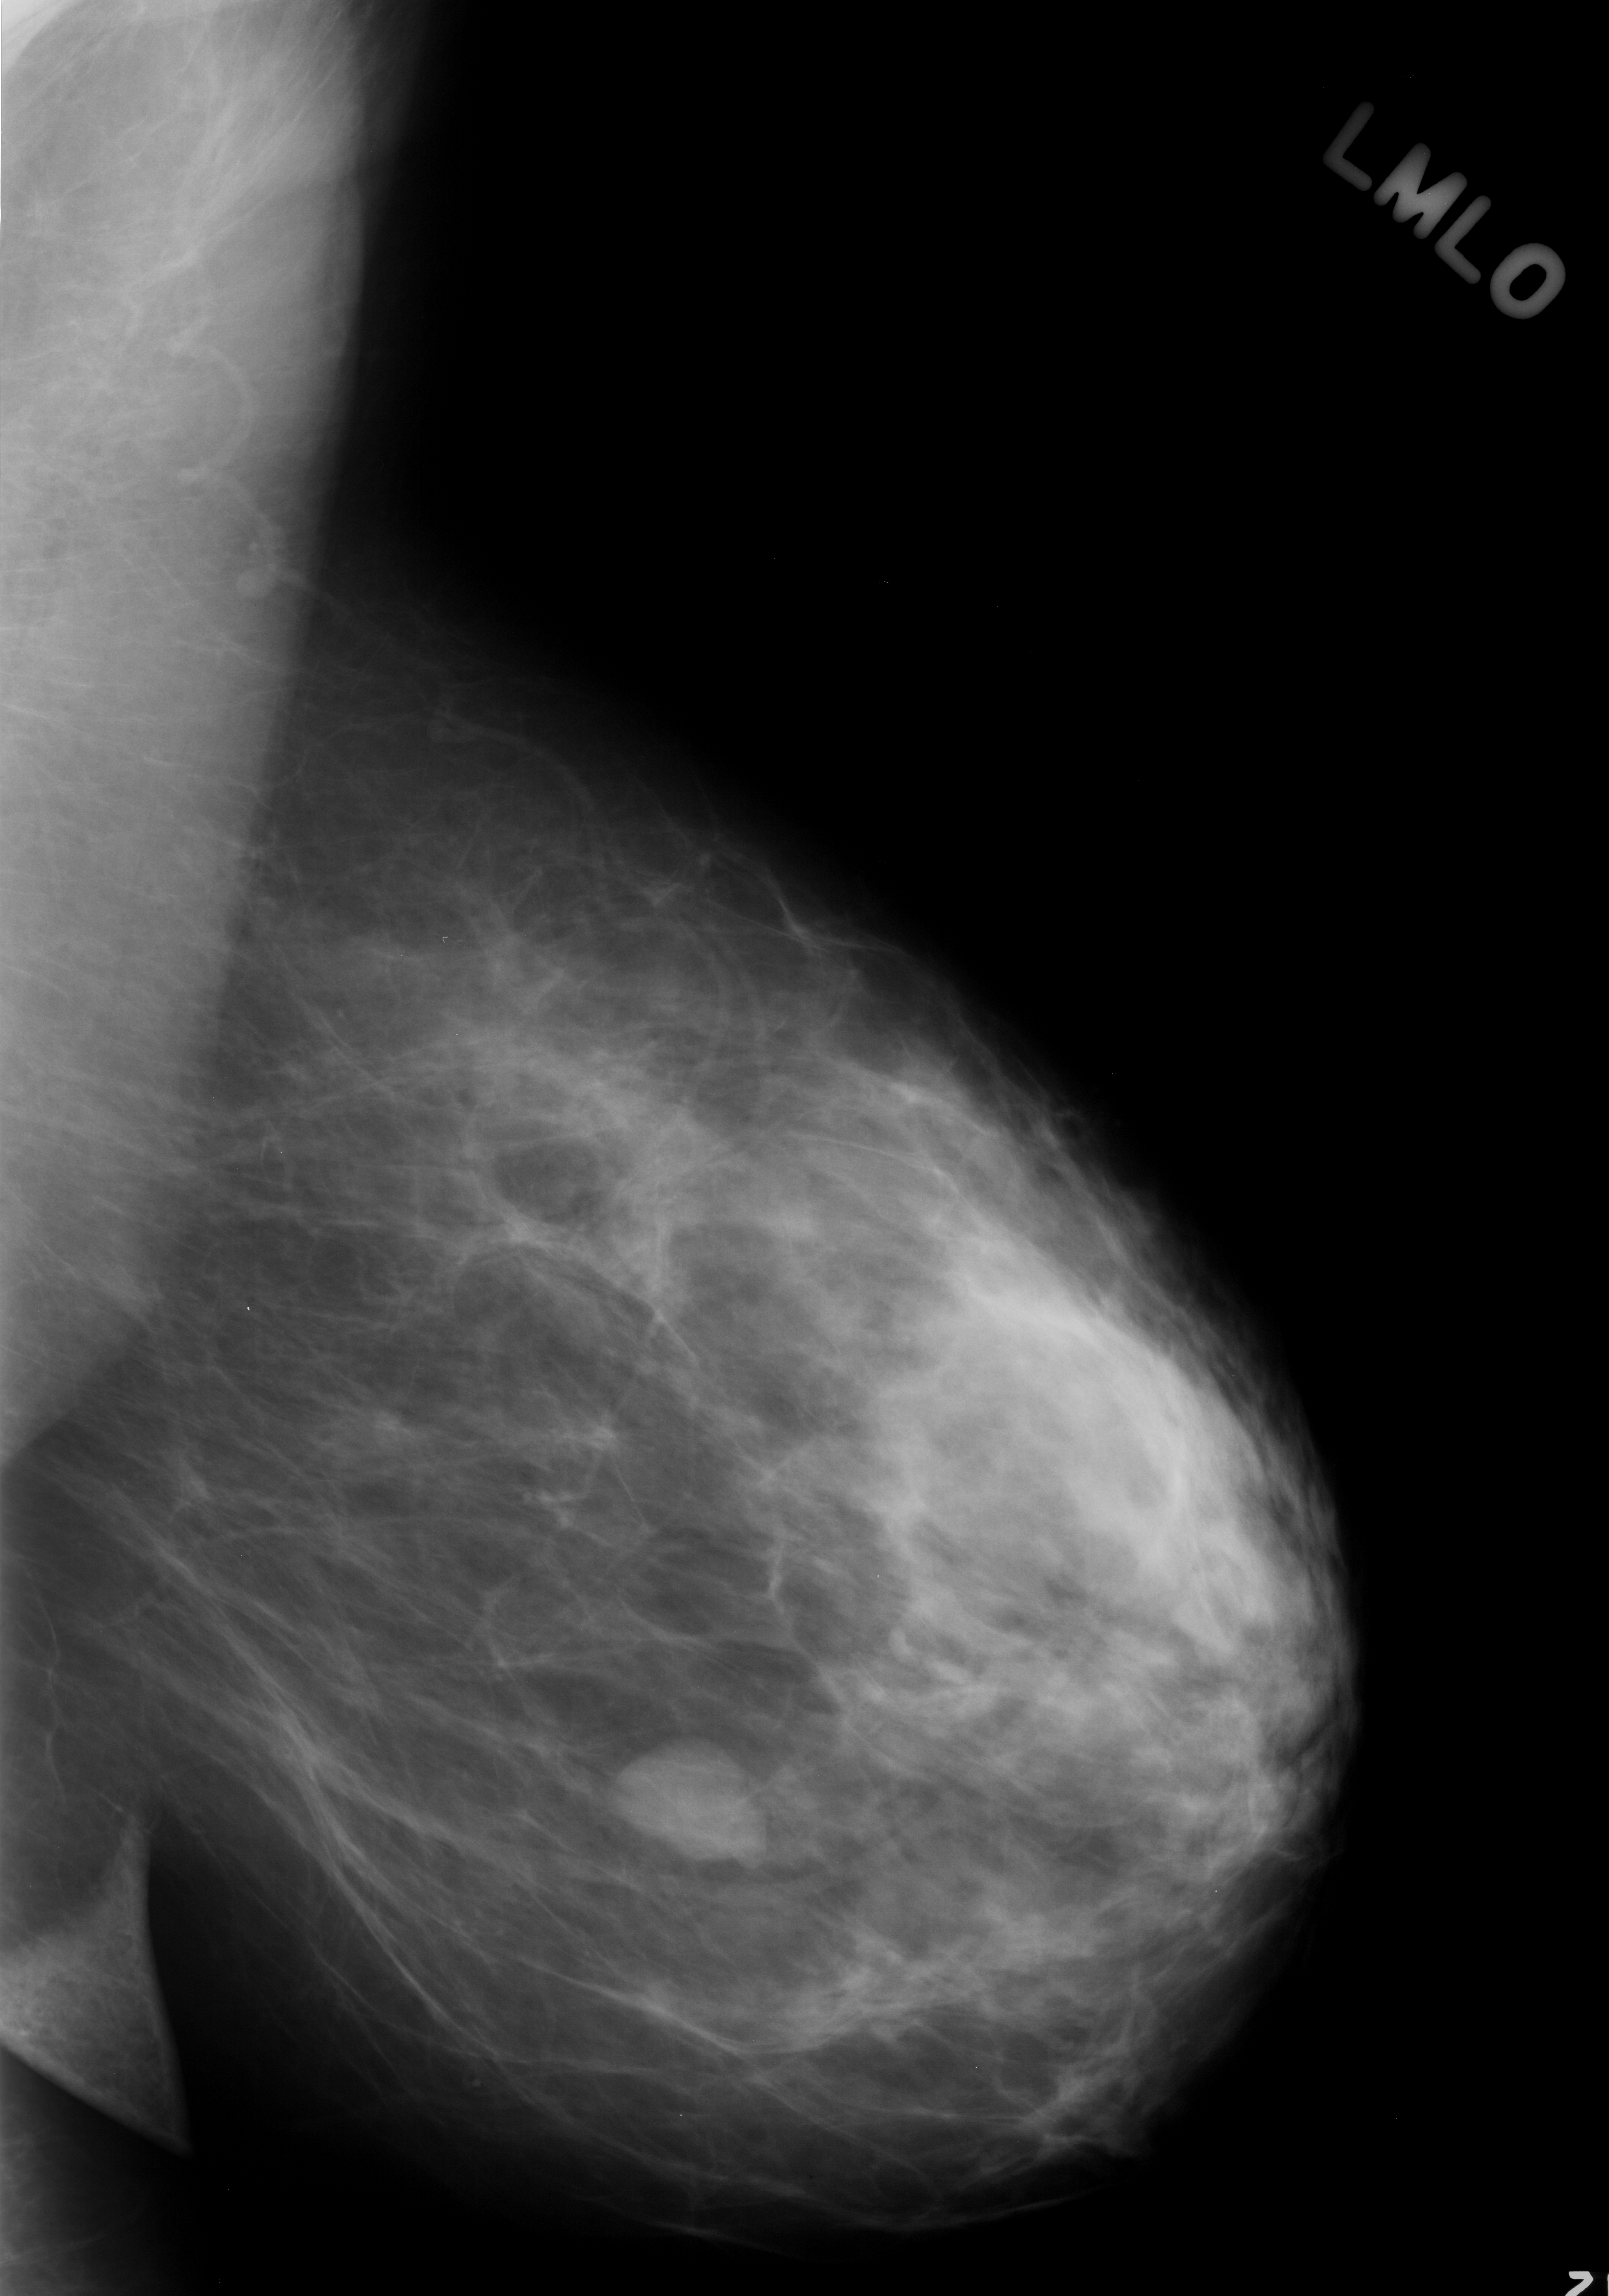
Mammogram (digitized film); left breast; MLO view; BI-RADS breast density category 2 (scale 1–4); 1609 × 2296 image matrix.
Expert-marked regions of interest on this film, with their recorded descriptors:
- mass, shape lobulated, margins circumscribed; BI-RADS assessment category 3; pathology result (as recorded, not read from the image): benign: box from (x=614, y=1737) to (x=761, y=1863) px